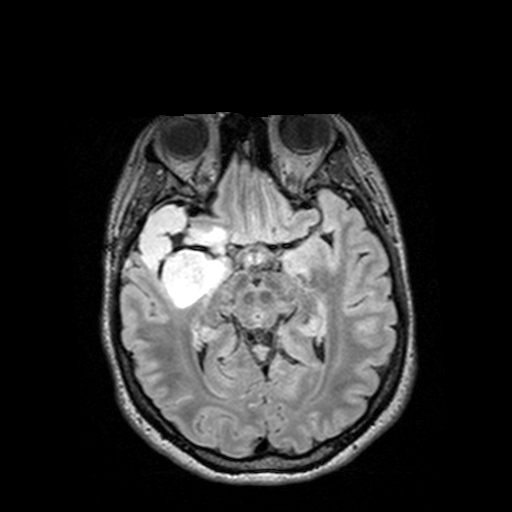
Brain MRI from a brain-tumour surgery series, one axial slice. Position 82 of 144 along the scan axis. T2 FLAIR. 1 mm slice thickness. 512 × 512 image matrix, field of view 250 × 250 mm. From the clinical record (not read from this slice): histopathology: Astrocytoma; WHO grade: 3; IDH mutation: yes; tumour location: Right Insular Temporal.
Structures marked on this image (outlined manually by an expert reader):
- tumour: bounding box [x1, y1, x2, y2] px = [126, 205, 232, 307]